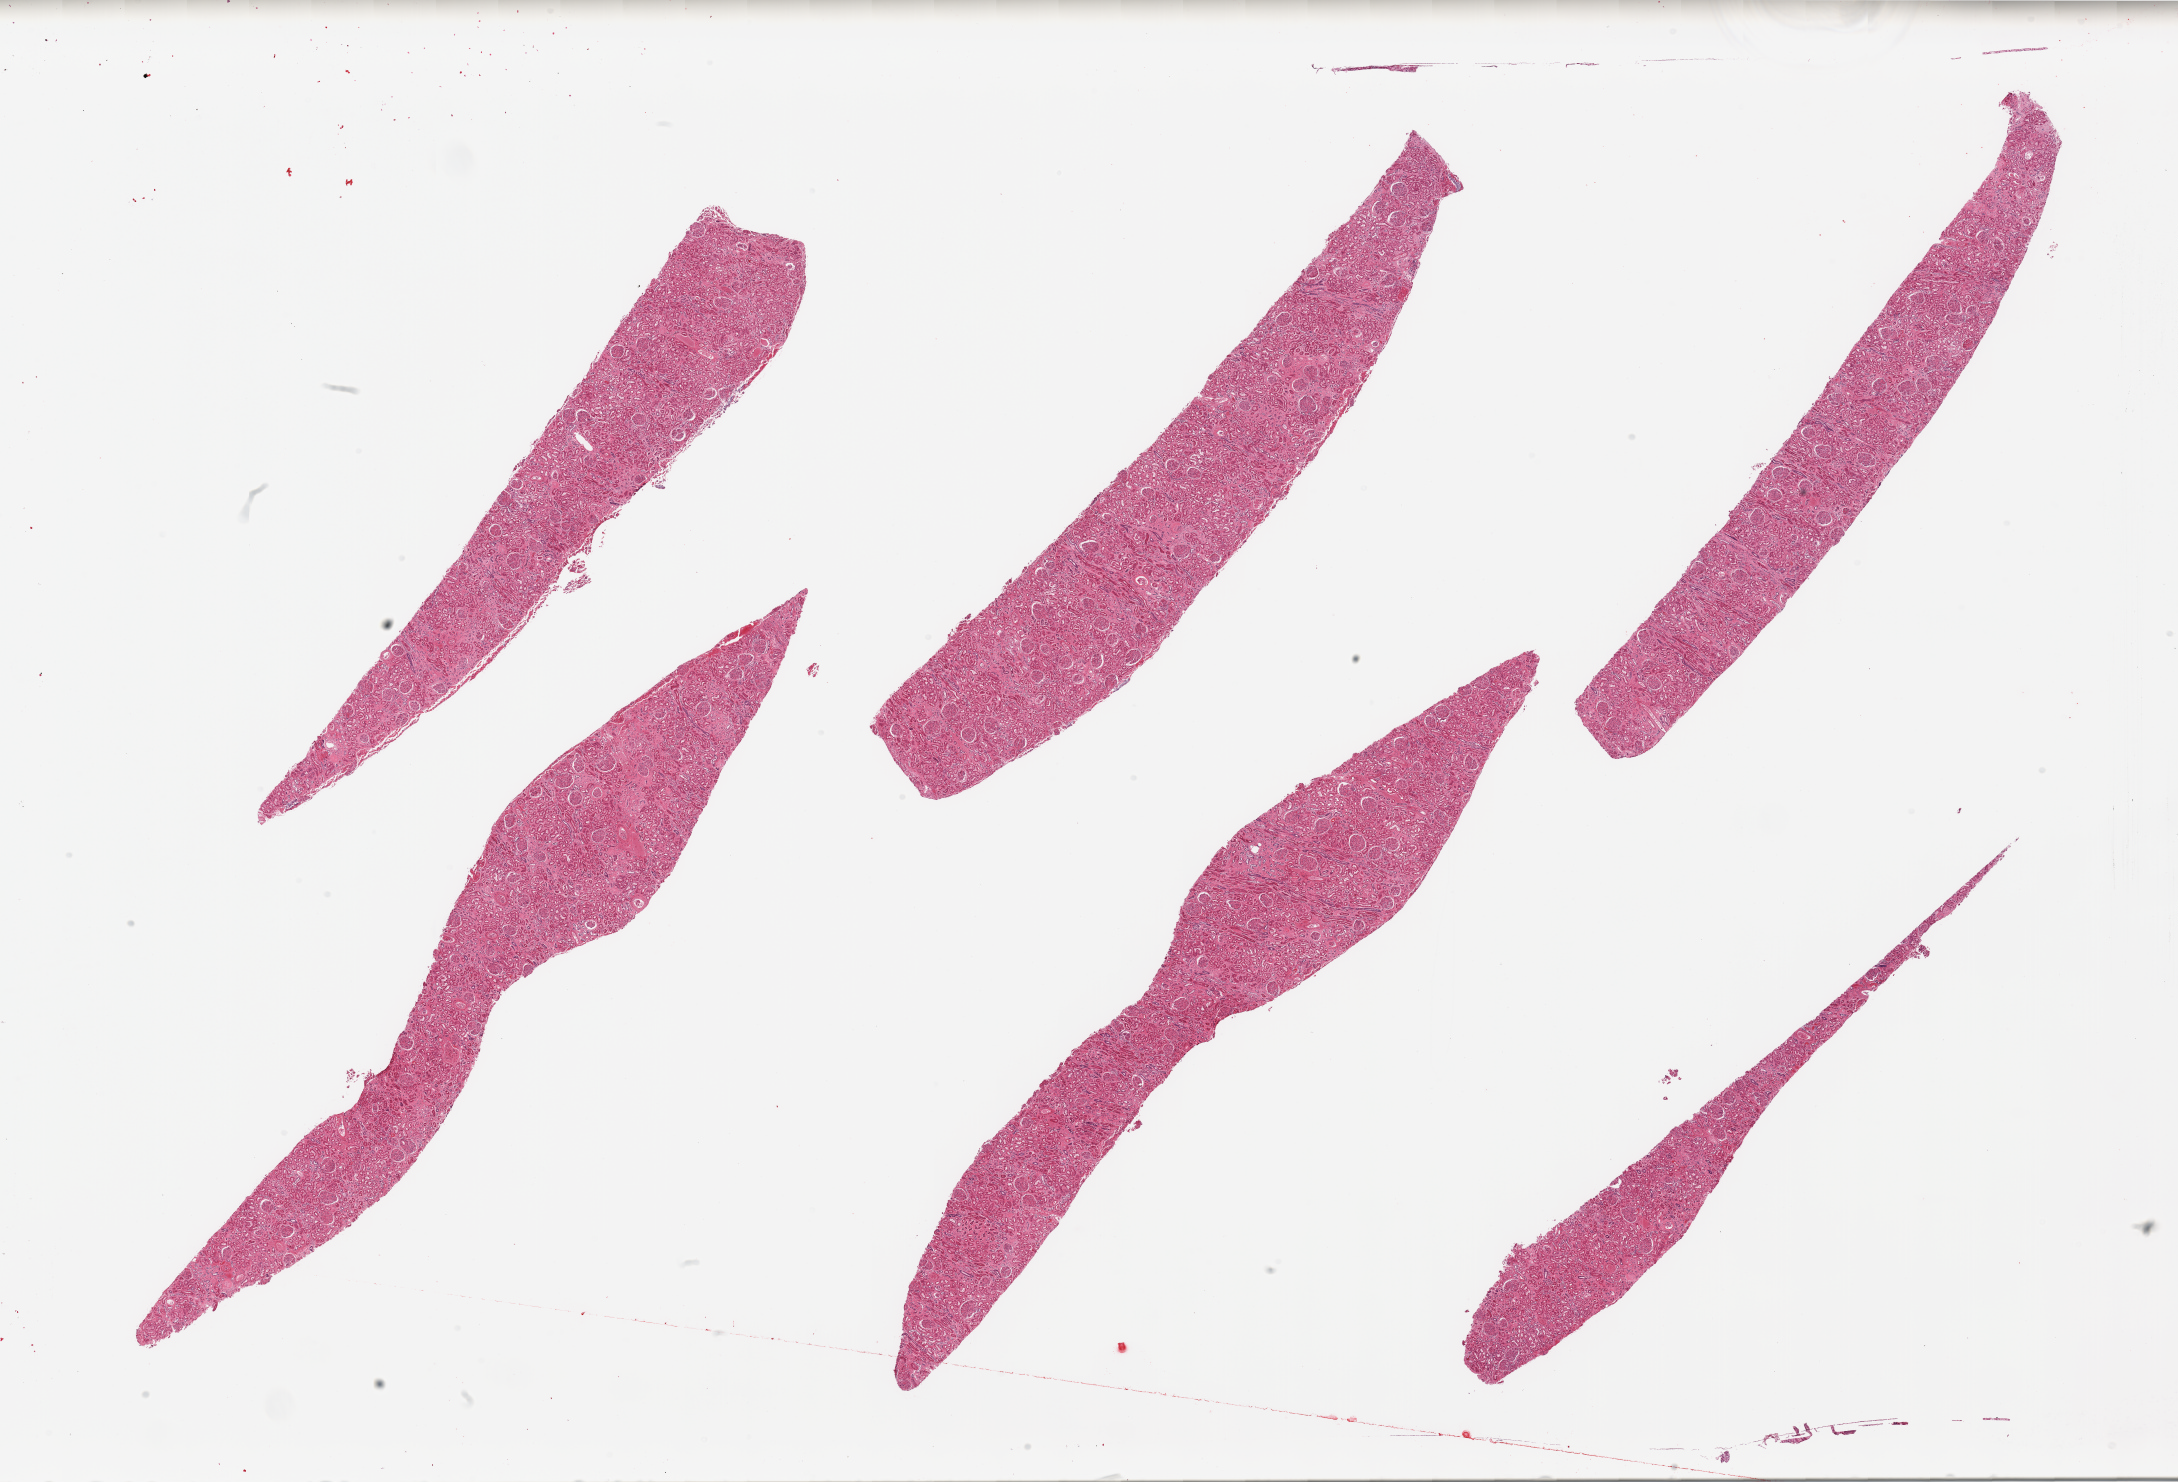
Digitized H&E-stained section, brightfield, shown as a low-resolution overview of the whole scanned area (about 34.5 x 23.4 mm, from a 20x scan); PAXgene-fixed, paraffin-embedded tissue; sampled site (target tissue): renal cortex; tissue donor sample.
• reviewer comment on this tissue sample: 6 pieces; focal intraglomerular sclerosis (diabetic type); arteriolar sclerosis